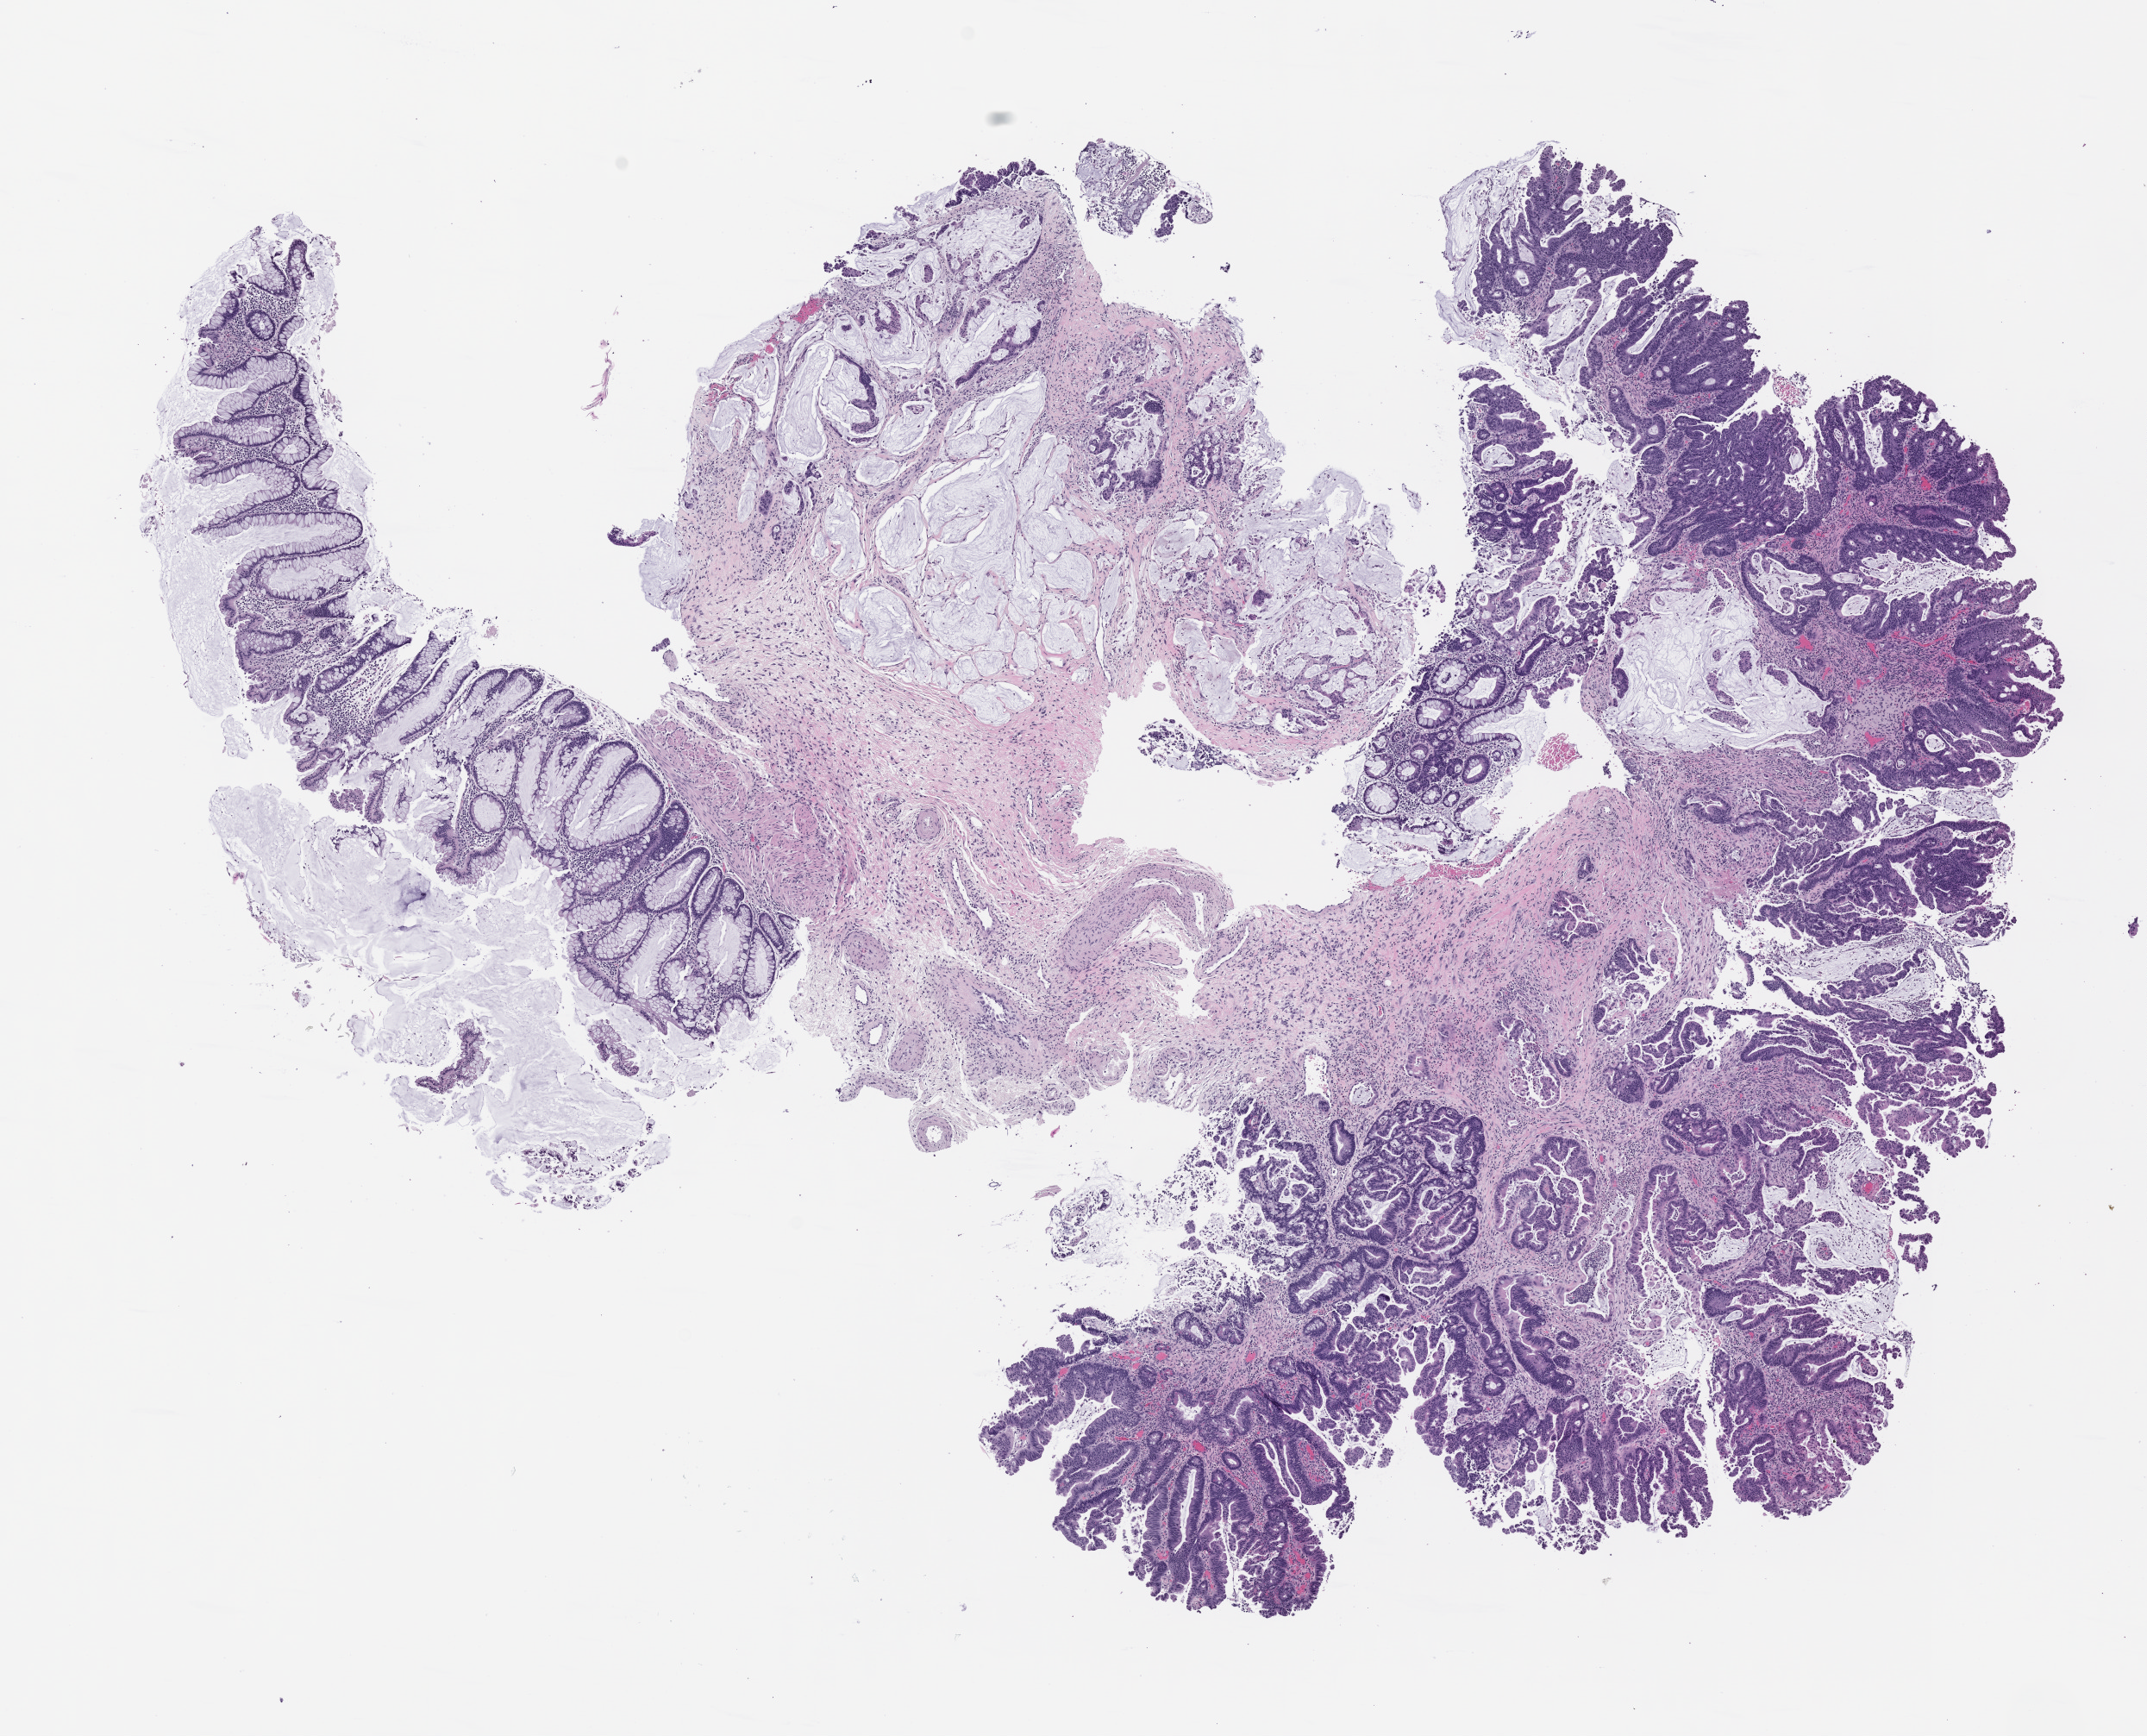
H&E whole-slide image of the patient's (originator) tumor tissue, low-resolution overview of the scanned area, about 10.0 x 8.1 mm; formalin-fixed, paraffin-embedded (FFPE) tissue; originating tumor site category: rectum. Male patient.
• diagnosis: Rectal Adenocarcinoma